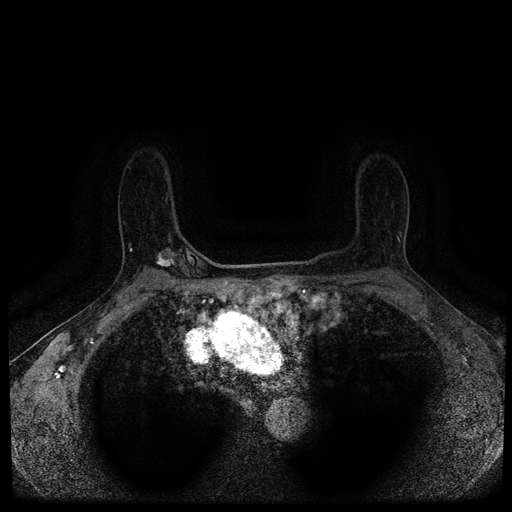
Breast MRI (dynamic contrast-enhanced, multi-phase), one axial slice. Slice 76 of 116 in the series (ordered by position). Dynamic contrast-enhanced series, time point 2 of 5 at this slice position (early post-contrast). 1.5 T. TE 2.7 ms, TR 5.4 ms. 512 × 512 image matrix. Patient: female, 63 years.
Outlined on this slice (semi-automatically segmented with operator editing):
- breast lesion (labelled 'tumour' in the annotation; benign lesions carry a separate 'benign' label): bounding box (x1, y1, x2, y2) in pixels: (155, 252, 180, 267)